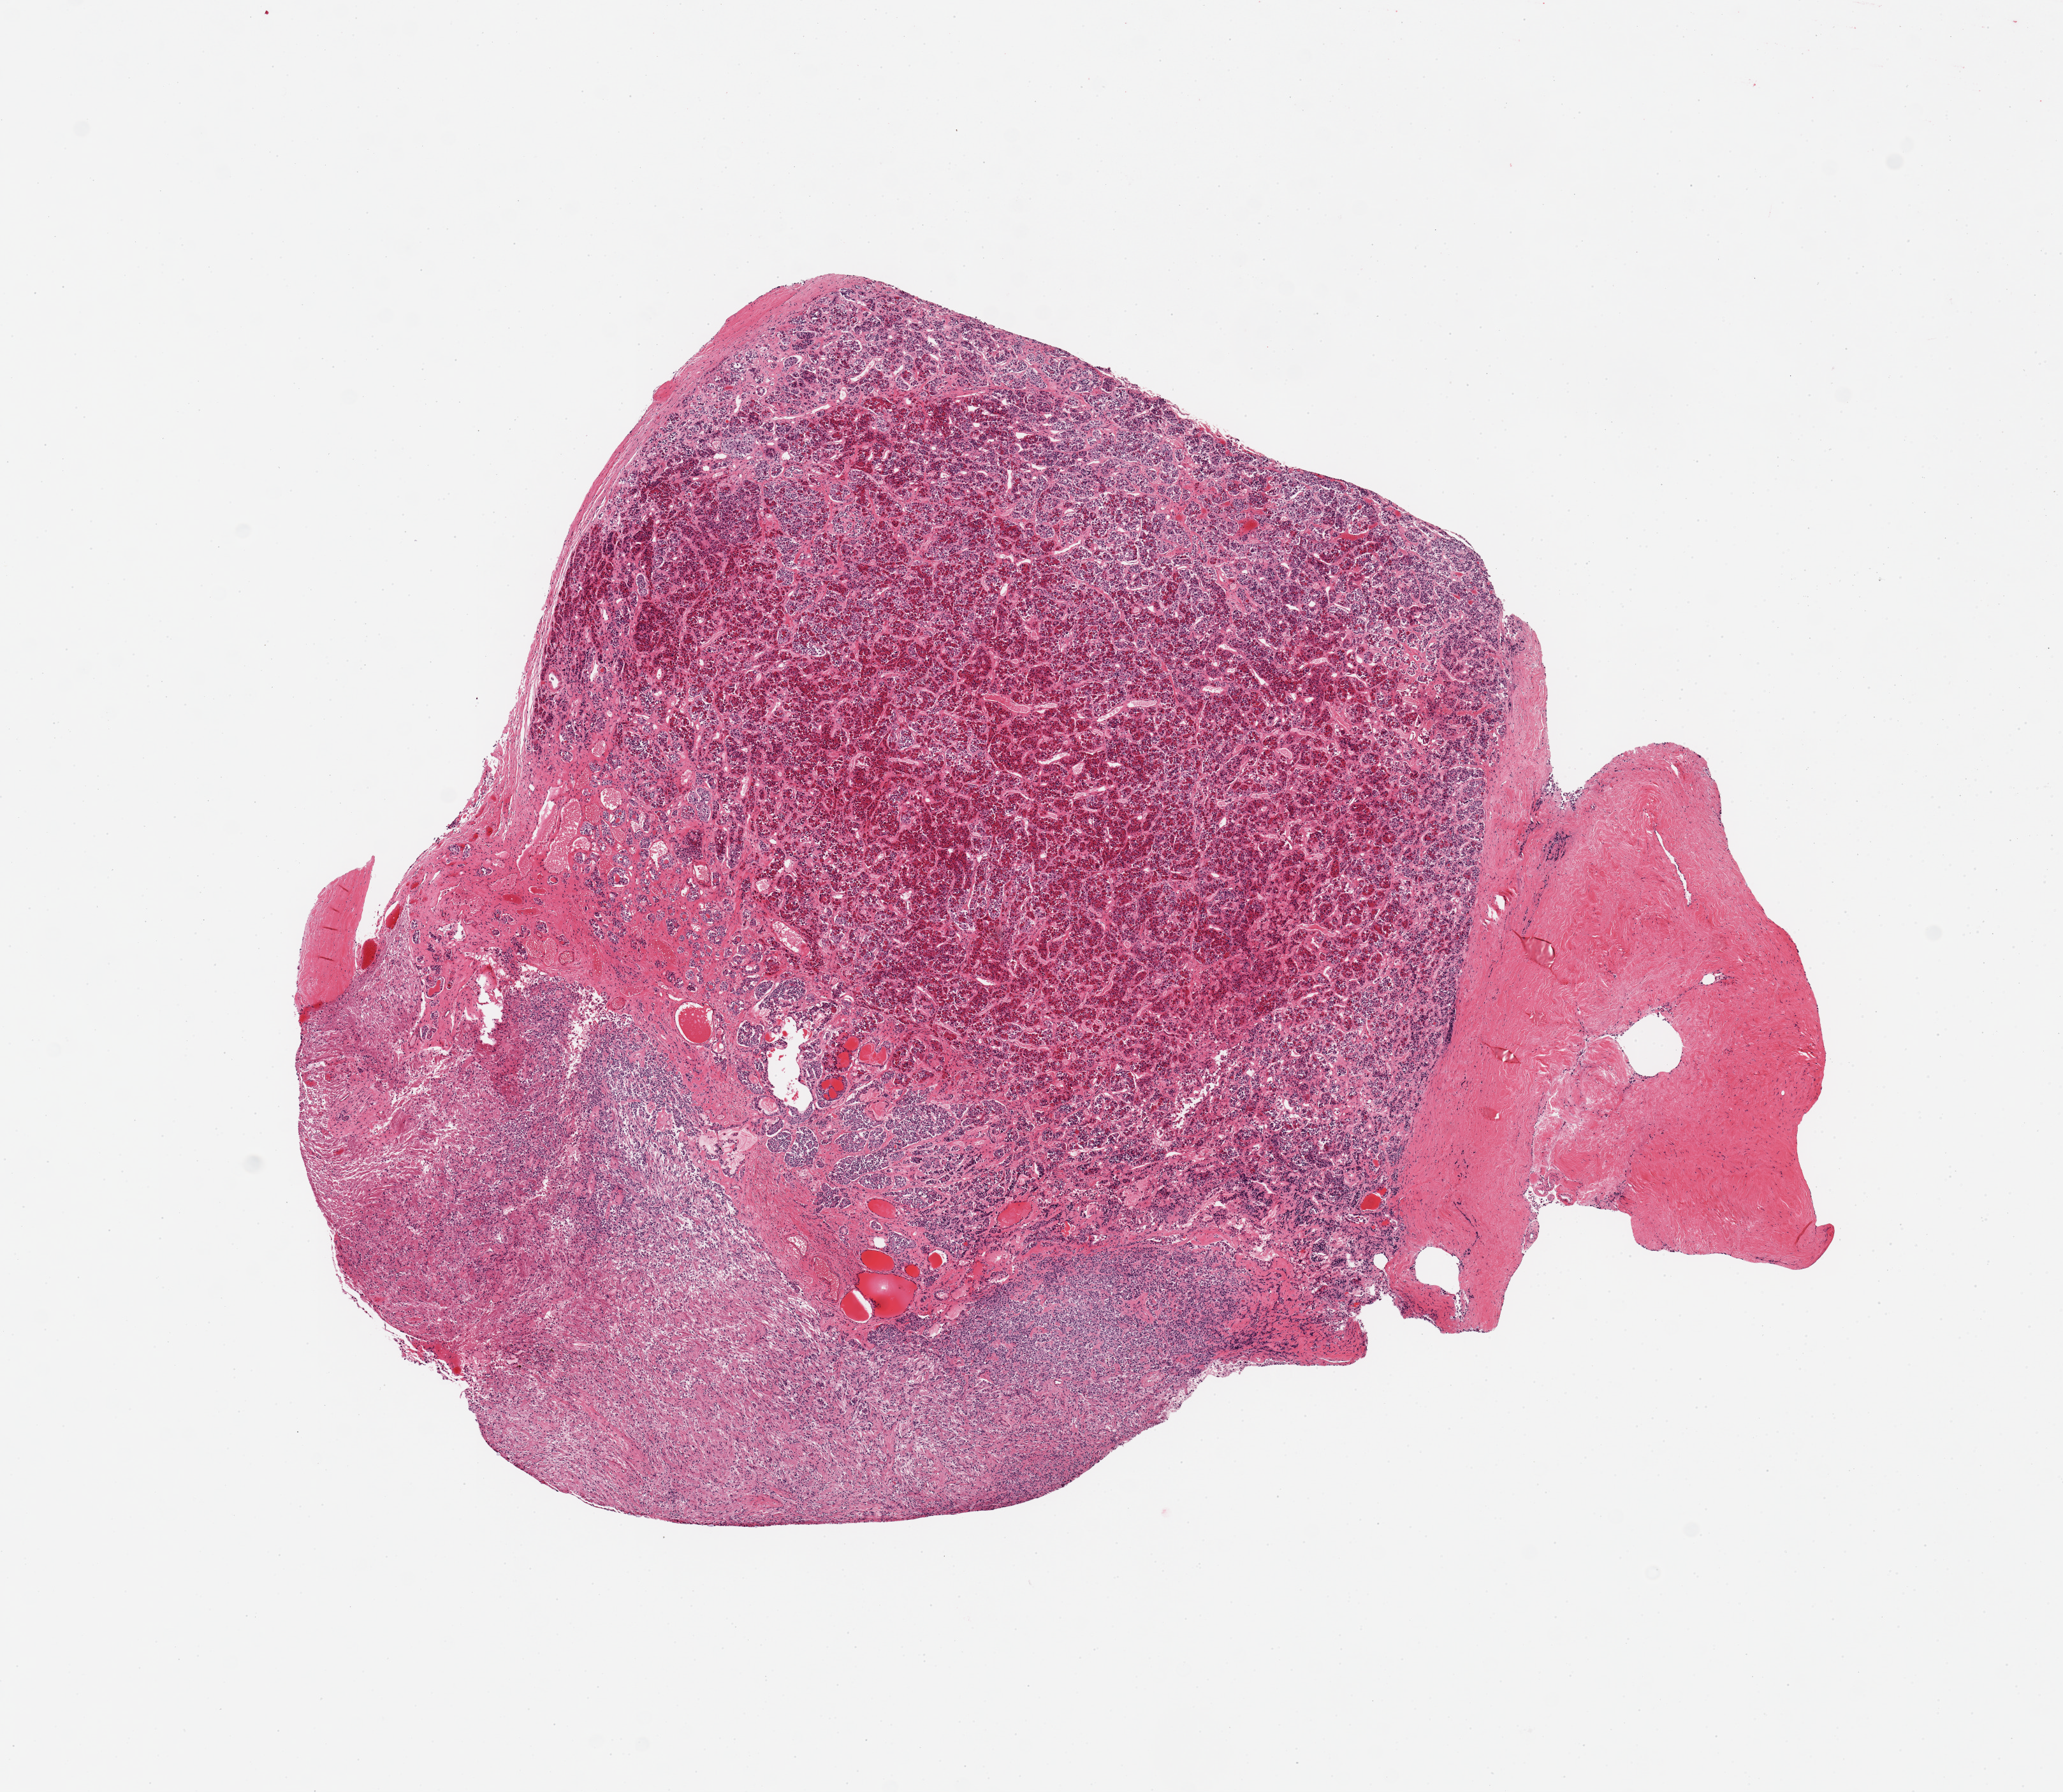
Whole-slide image, hematoxylin and eosin (H&E) stain, whole scanned area (about 12.8 x 11.1 mm) shown as a low-resolution overview. PAXgene-fixed, paraffin-embedded tissue. Sampled site (target tissue): pituitary. Tissue donor sample. Male donor.
• pathologist's review note for this sample: 1 piece; 55% adenohypophysis, 30% neurohypophysis, and 15% congested dense fibrous tissue